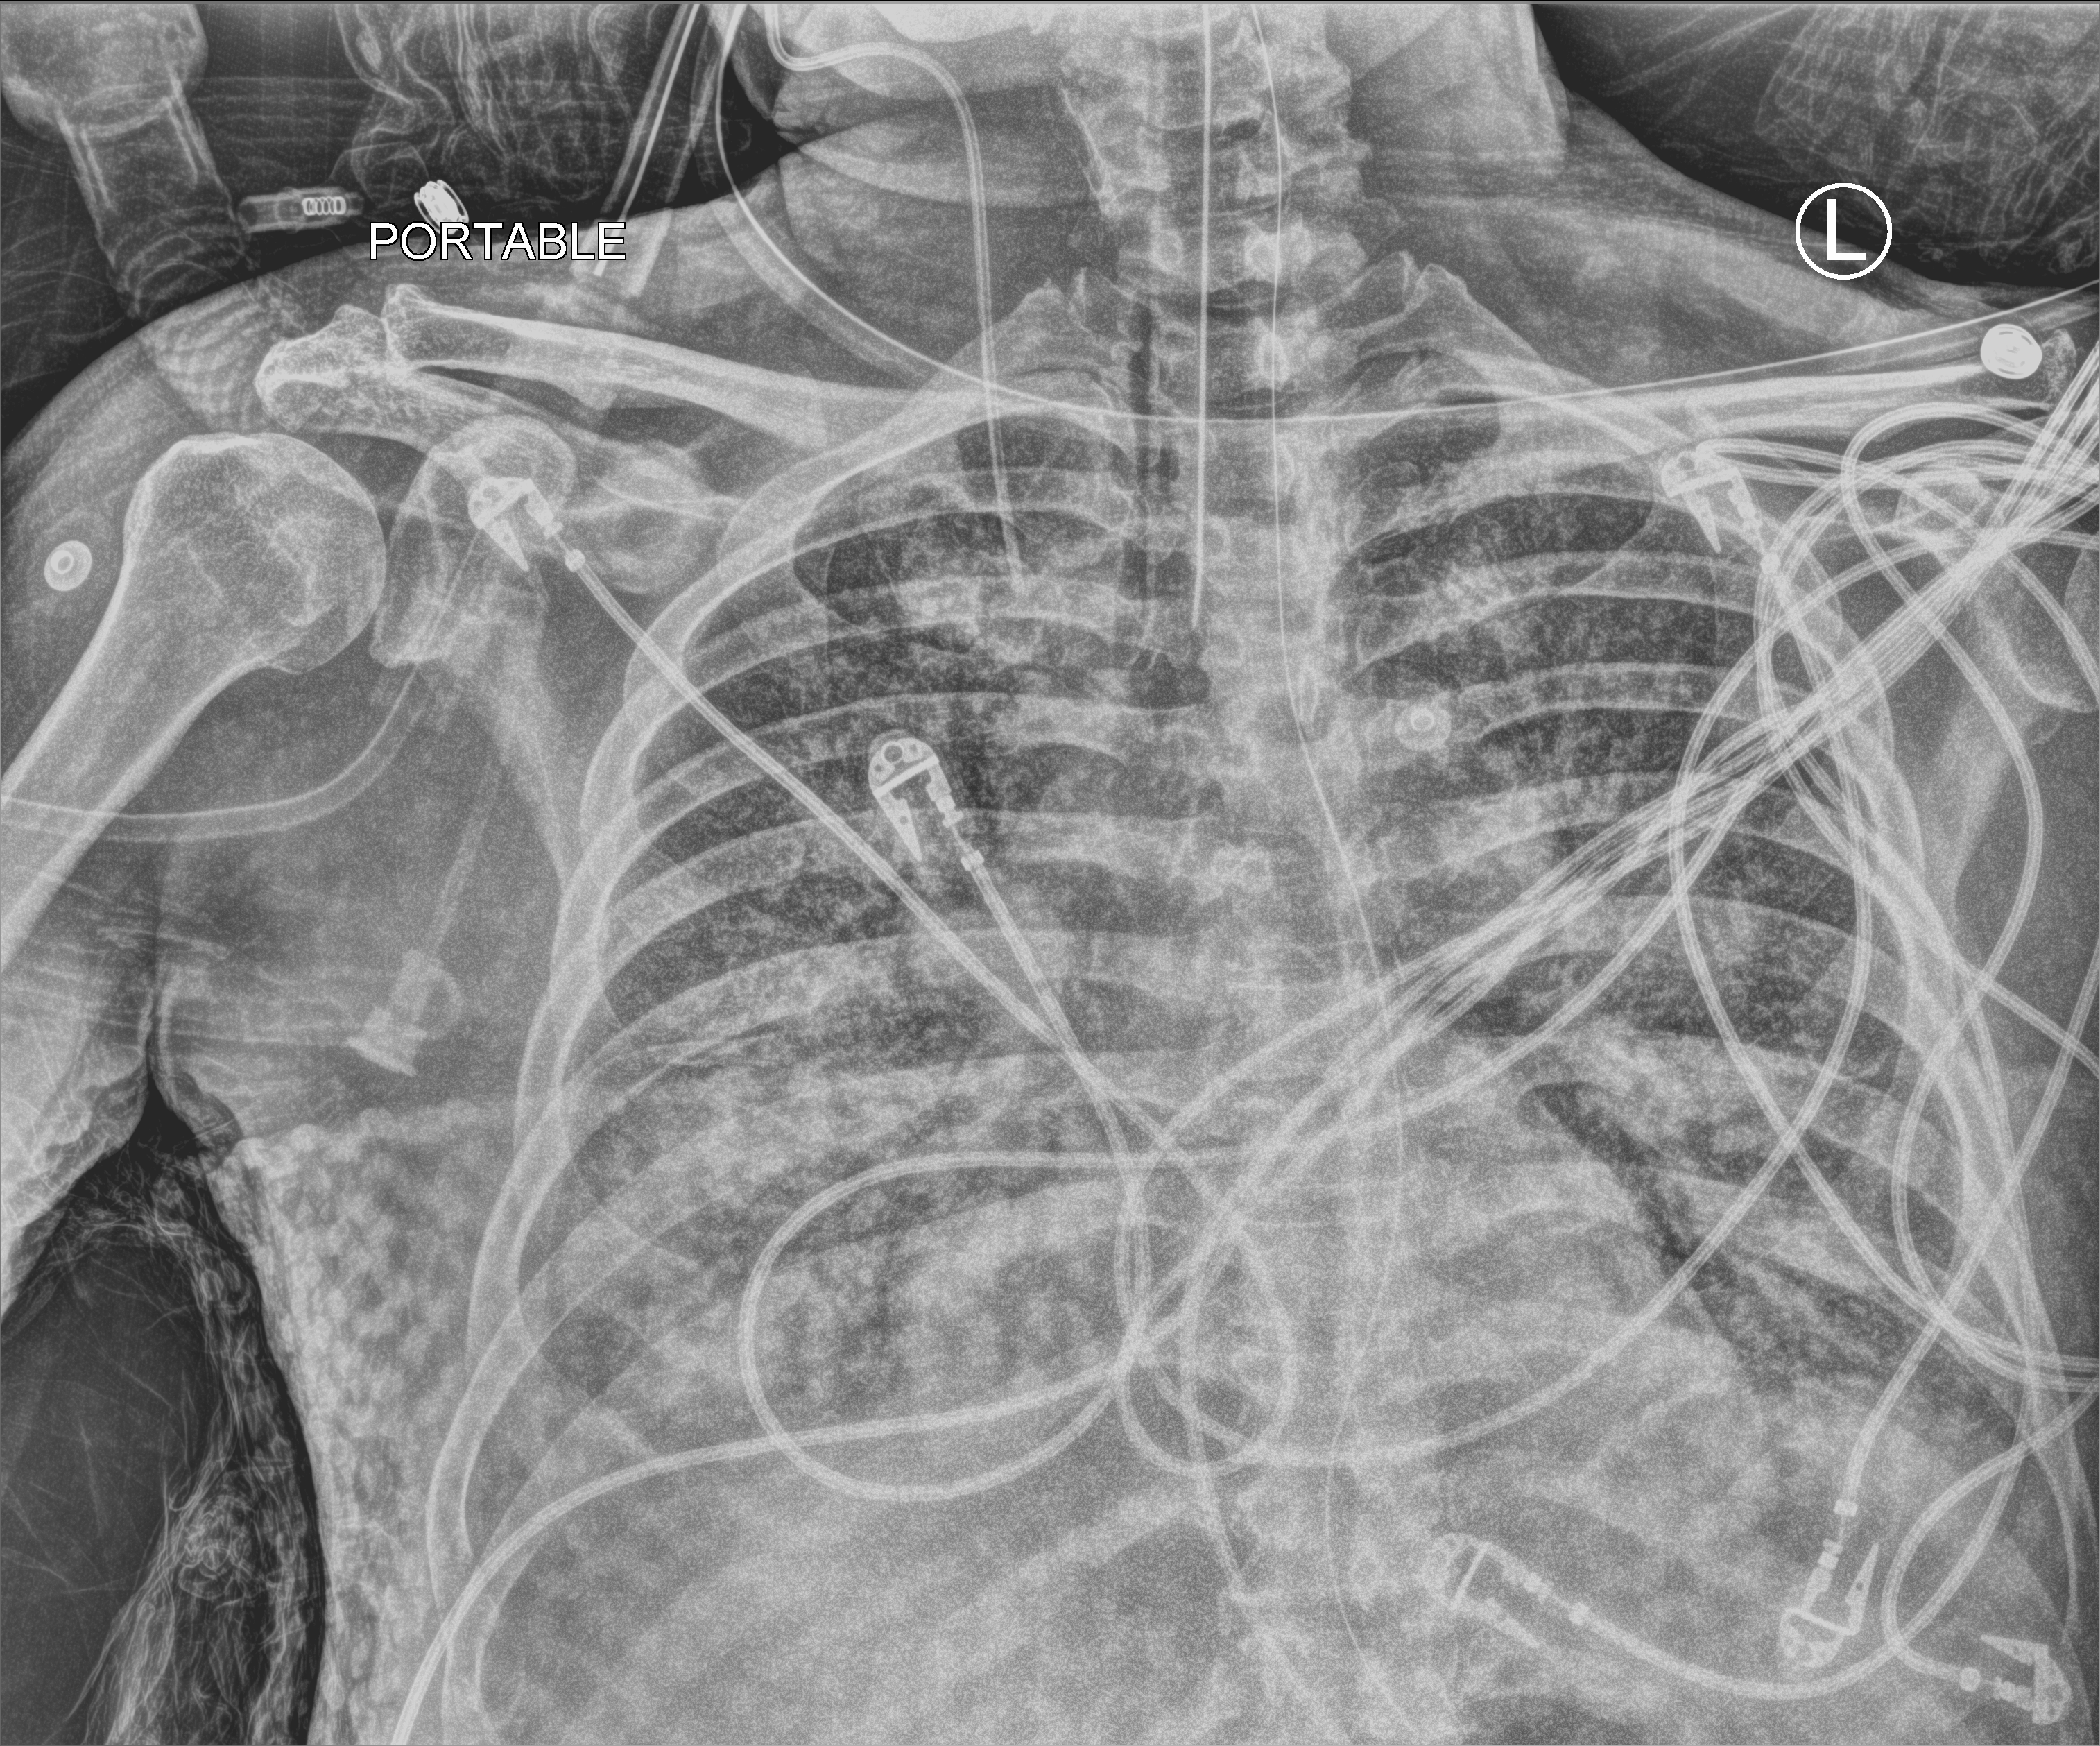
Portable chest radiograph, anteroposterior (AP) projection. Male patient hospitalised with COVID-19, age 60–74 years.
From the hospital-stay record, not from the radiograph (when in the stay this image was taken is not recorded): hypertension (admission record): yes.